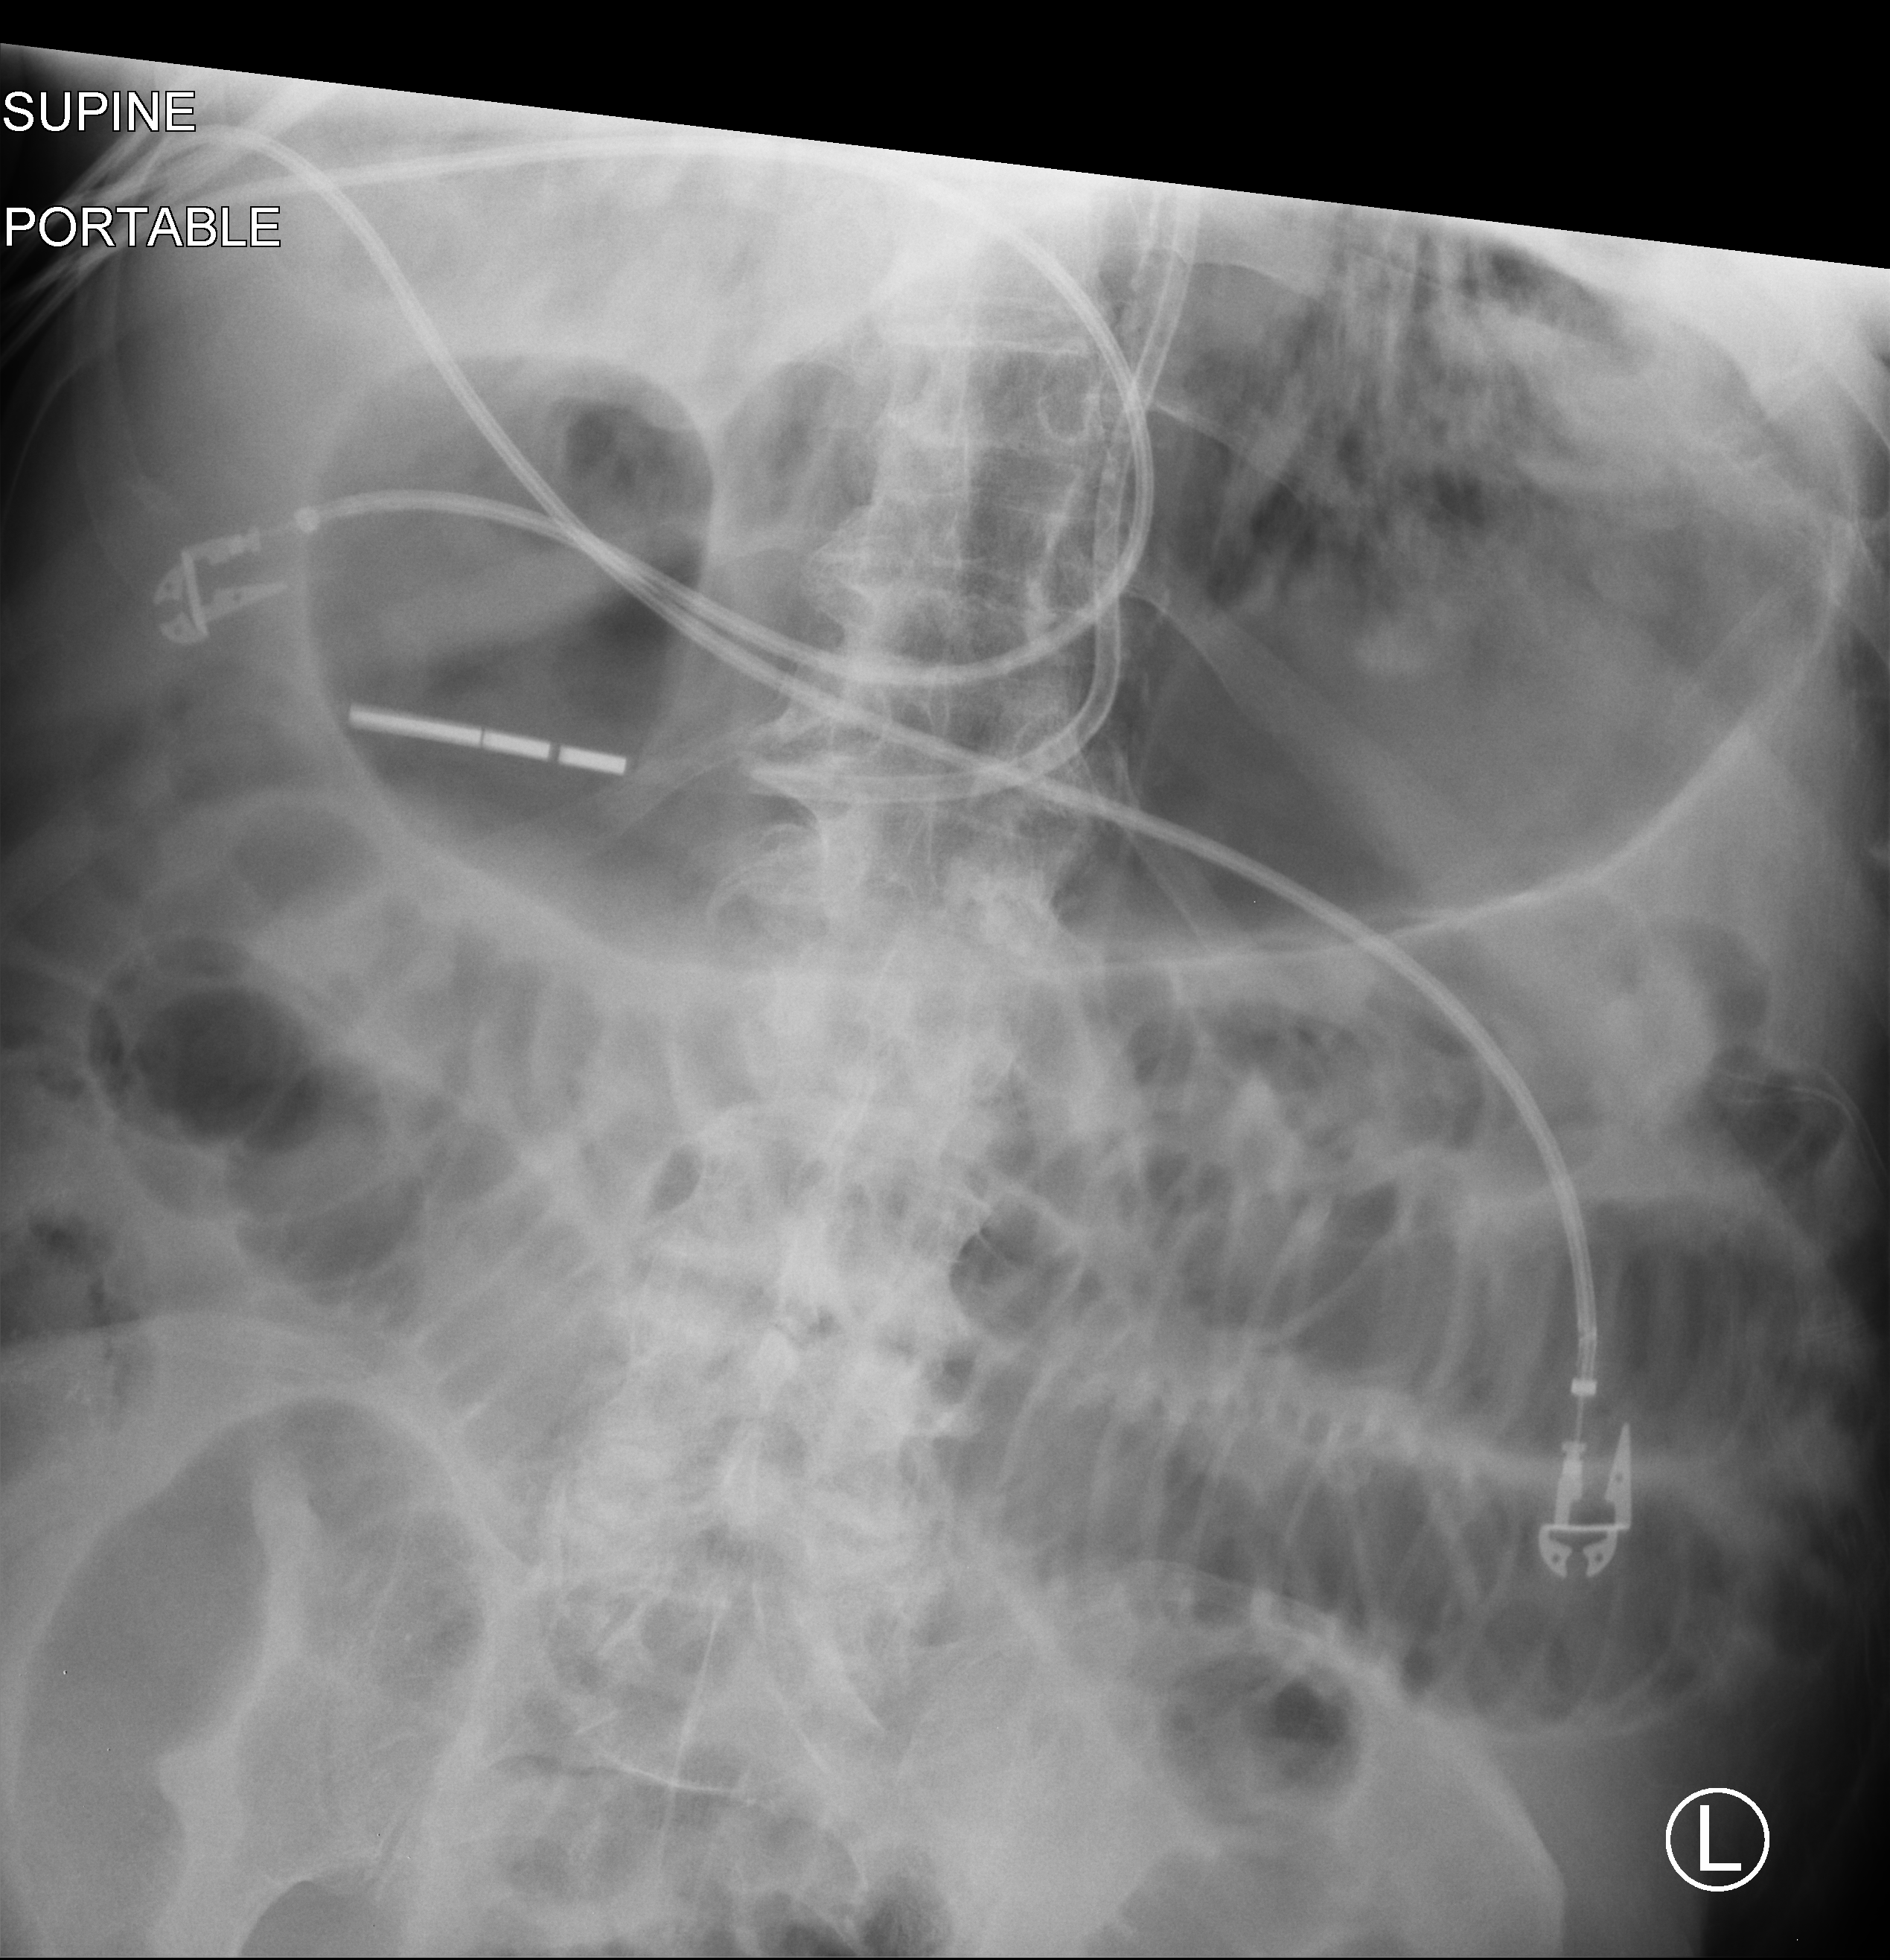
Portable abdomen radiograph, anteroposterior (AP) projection. Male patient hospitalised with COVID-19, age 75–90 years.
Hospital-stay facts (about this admission, not read from this image; timing relative to this image not recorded): smoking status (admission record): former; mechanically ventilated during this hospital stay: yes.